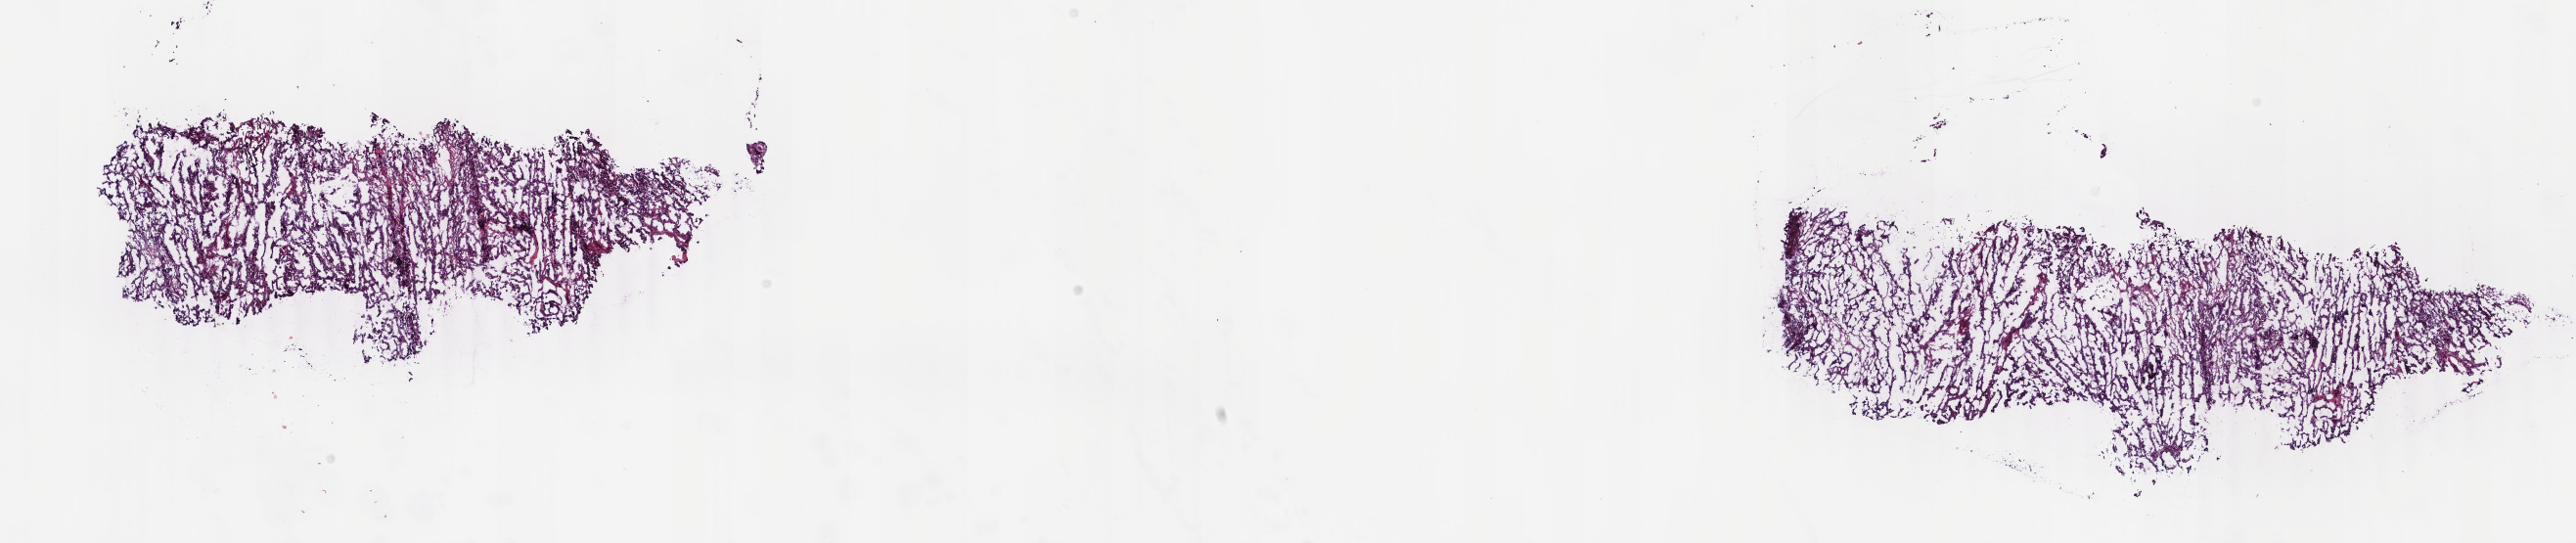
Digitized H&E tissue section (whole slide), whole scanned area (about 20.9 x 4.4 mm, acquisition: 40x scan) shown as a low-resolution overview, frozen section from the top of the tissue portion, uterus, primary tumour sample. Female, age 59 years at initial diagnosis. Histologic grade: G3 (poorly differentiated). Composition of this section per pathologist review: tumour cells 83%, tumour nuclei 85%, normal cells 0%, stromal cells 15%, necrosis 2%. Inflammatory infiltration, as recorded: lymphocyte infiltration 3%, monocyte infiltration 1%, neutrophil infiltration 0%.
Histologic diagnosis: Serous cystadenocarcinoma, NOS (endometrium). FIGO stage: IVB.